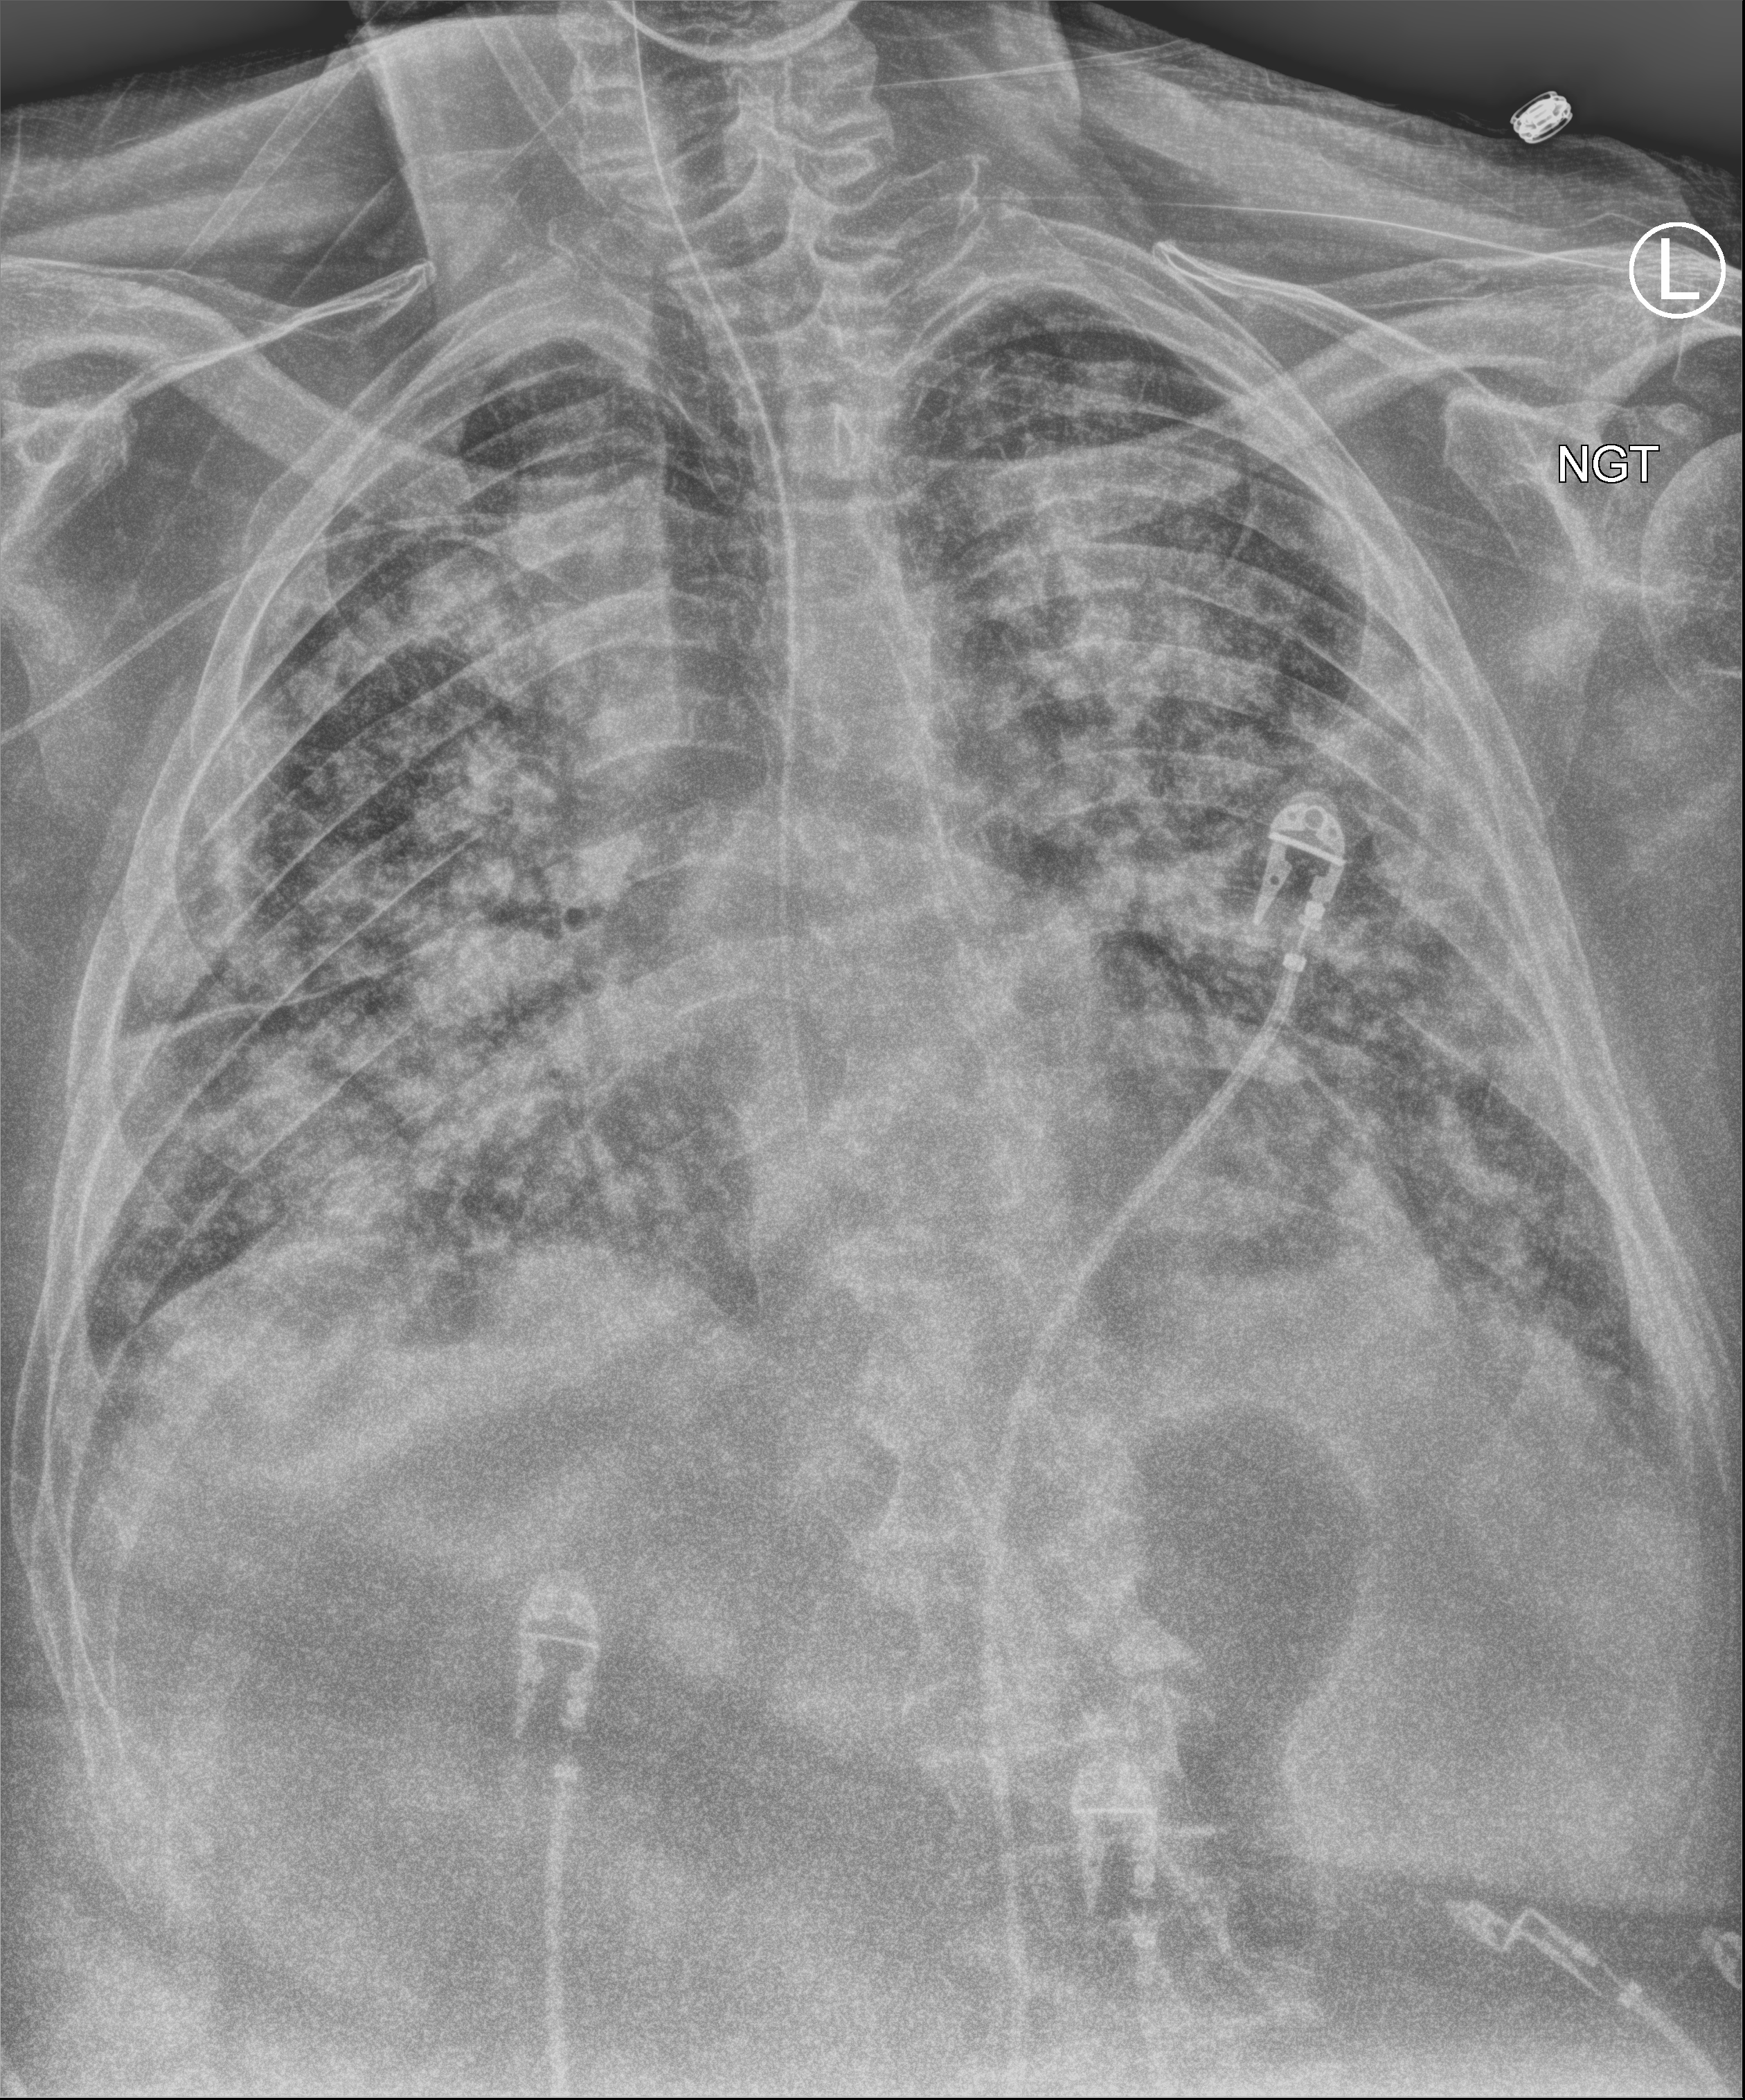
Portable chest radiograph; anteroposterior (AP) projection. Male patient hospitalised with COVID-19, age 60–74 years.
From the hospital-stay record, not from the radiograph (when in the stay this image was taken is not recorded): diabetes (admission record): yes; admitted to intensive care during this hospital stay: yes.